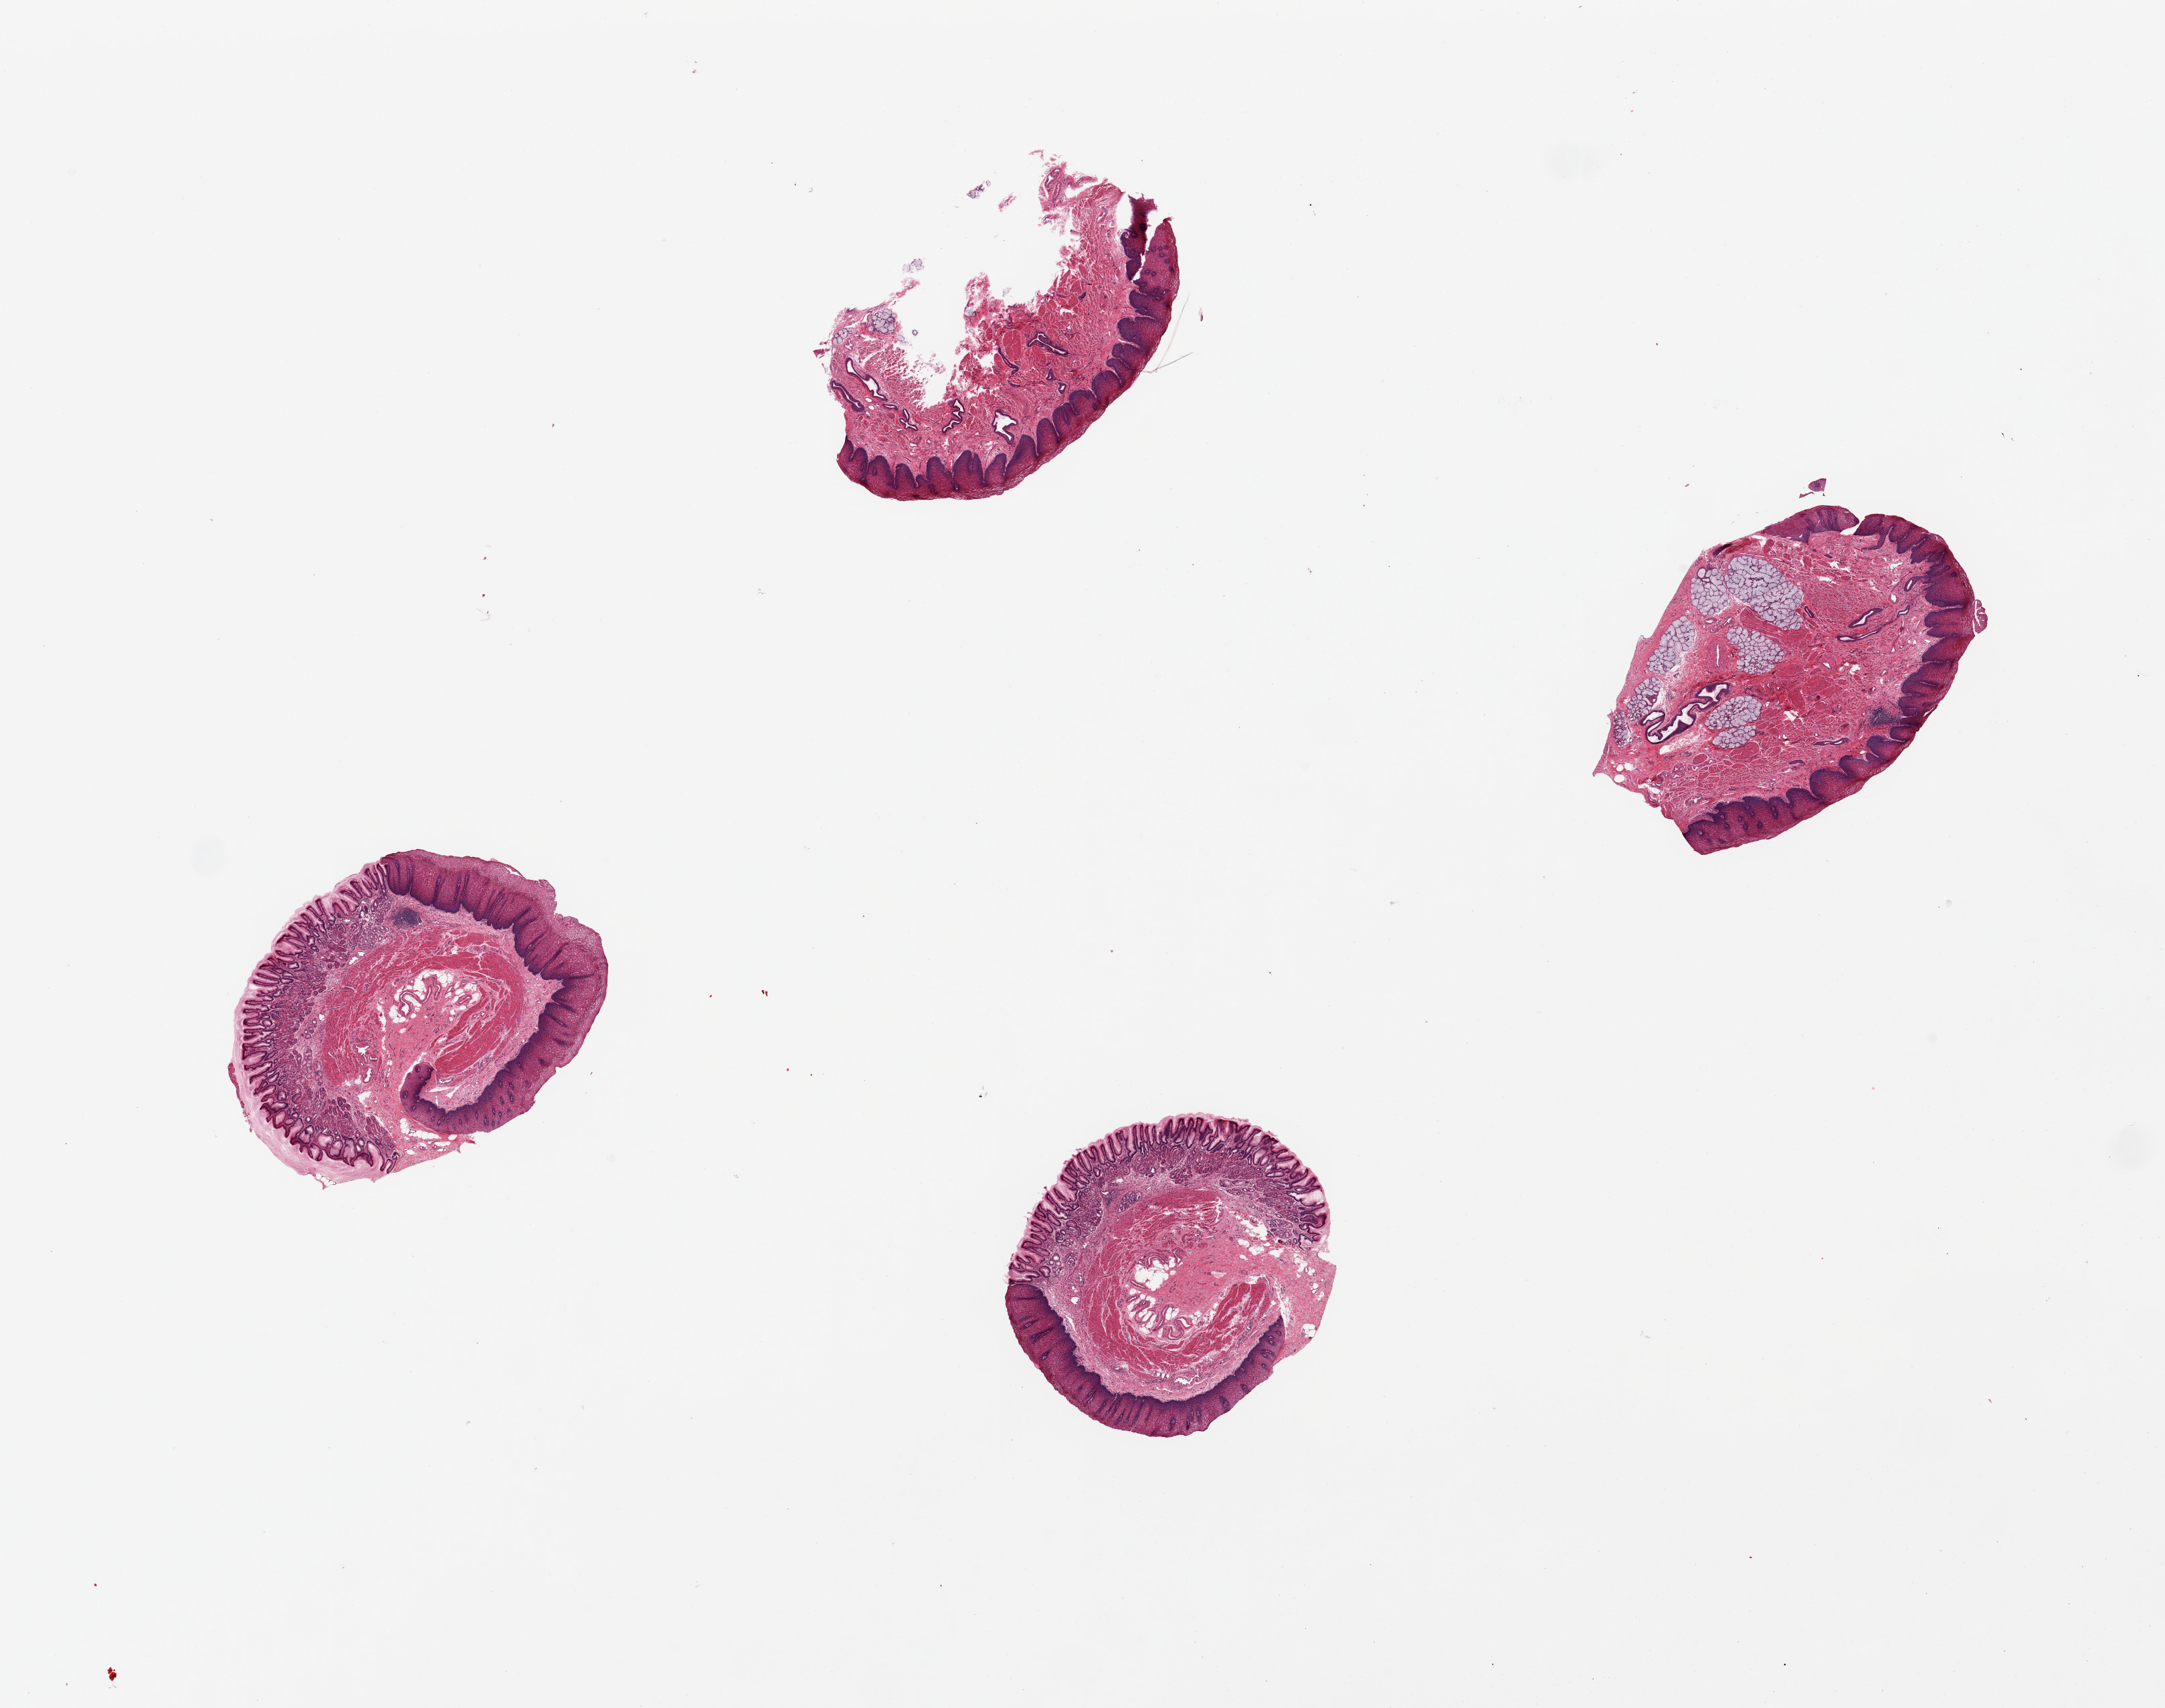
H&E whole-slide image — a low-resolution overview of the entire scanned area, about 25.6 x 20.2 mm (acquisition: 20x scan), PAXgene-fixed, paraffin-embedded tissue, sampled site (target tissue): esophageal mucous membrane, tissue donor sample. Female donor.
Pathologist's review note for this sample: 4 pieces, 2 include gastric cardiac mucosa.